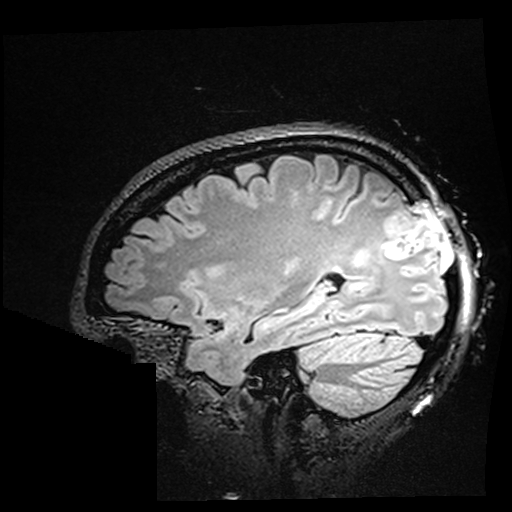
Brain MRI from a brain-tumour surgery series, one sagittal slice. Position 121 of 176 along the scan axis. T2 FLAIR. 512 × 512 image matrix, field of view 250 × 250 mm. Case-level facts recorded for this patient, not image findings: histopathology: Oligodendroglioma; WHO grade: 2; IDH mutation: yes.
Structures marked on this image (outlined manually by an expert reader):
- residual tumour: box from (x=355, y=251) to (x=366, y=261) px